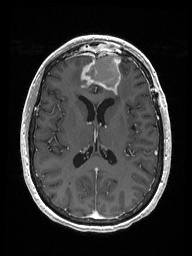
Brain MRI from a brain-tumour surgery series, one axial slice; position 76 of 192 along the scan axis; T1-weighted post-contrast; 1 mm slice thickness; 192 × 256 image matrix, field of view 187 × 250 mm. From the clinical record (not read from this slice): histopathology: Metastastic Carcinoma from Breast primary; tumour location: Right Frontal.
Outlined on this slice (expert manual segmentation):
- previous resection cavity: box from (x=87, y=52) to (x=121, y=88) px